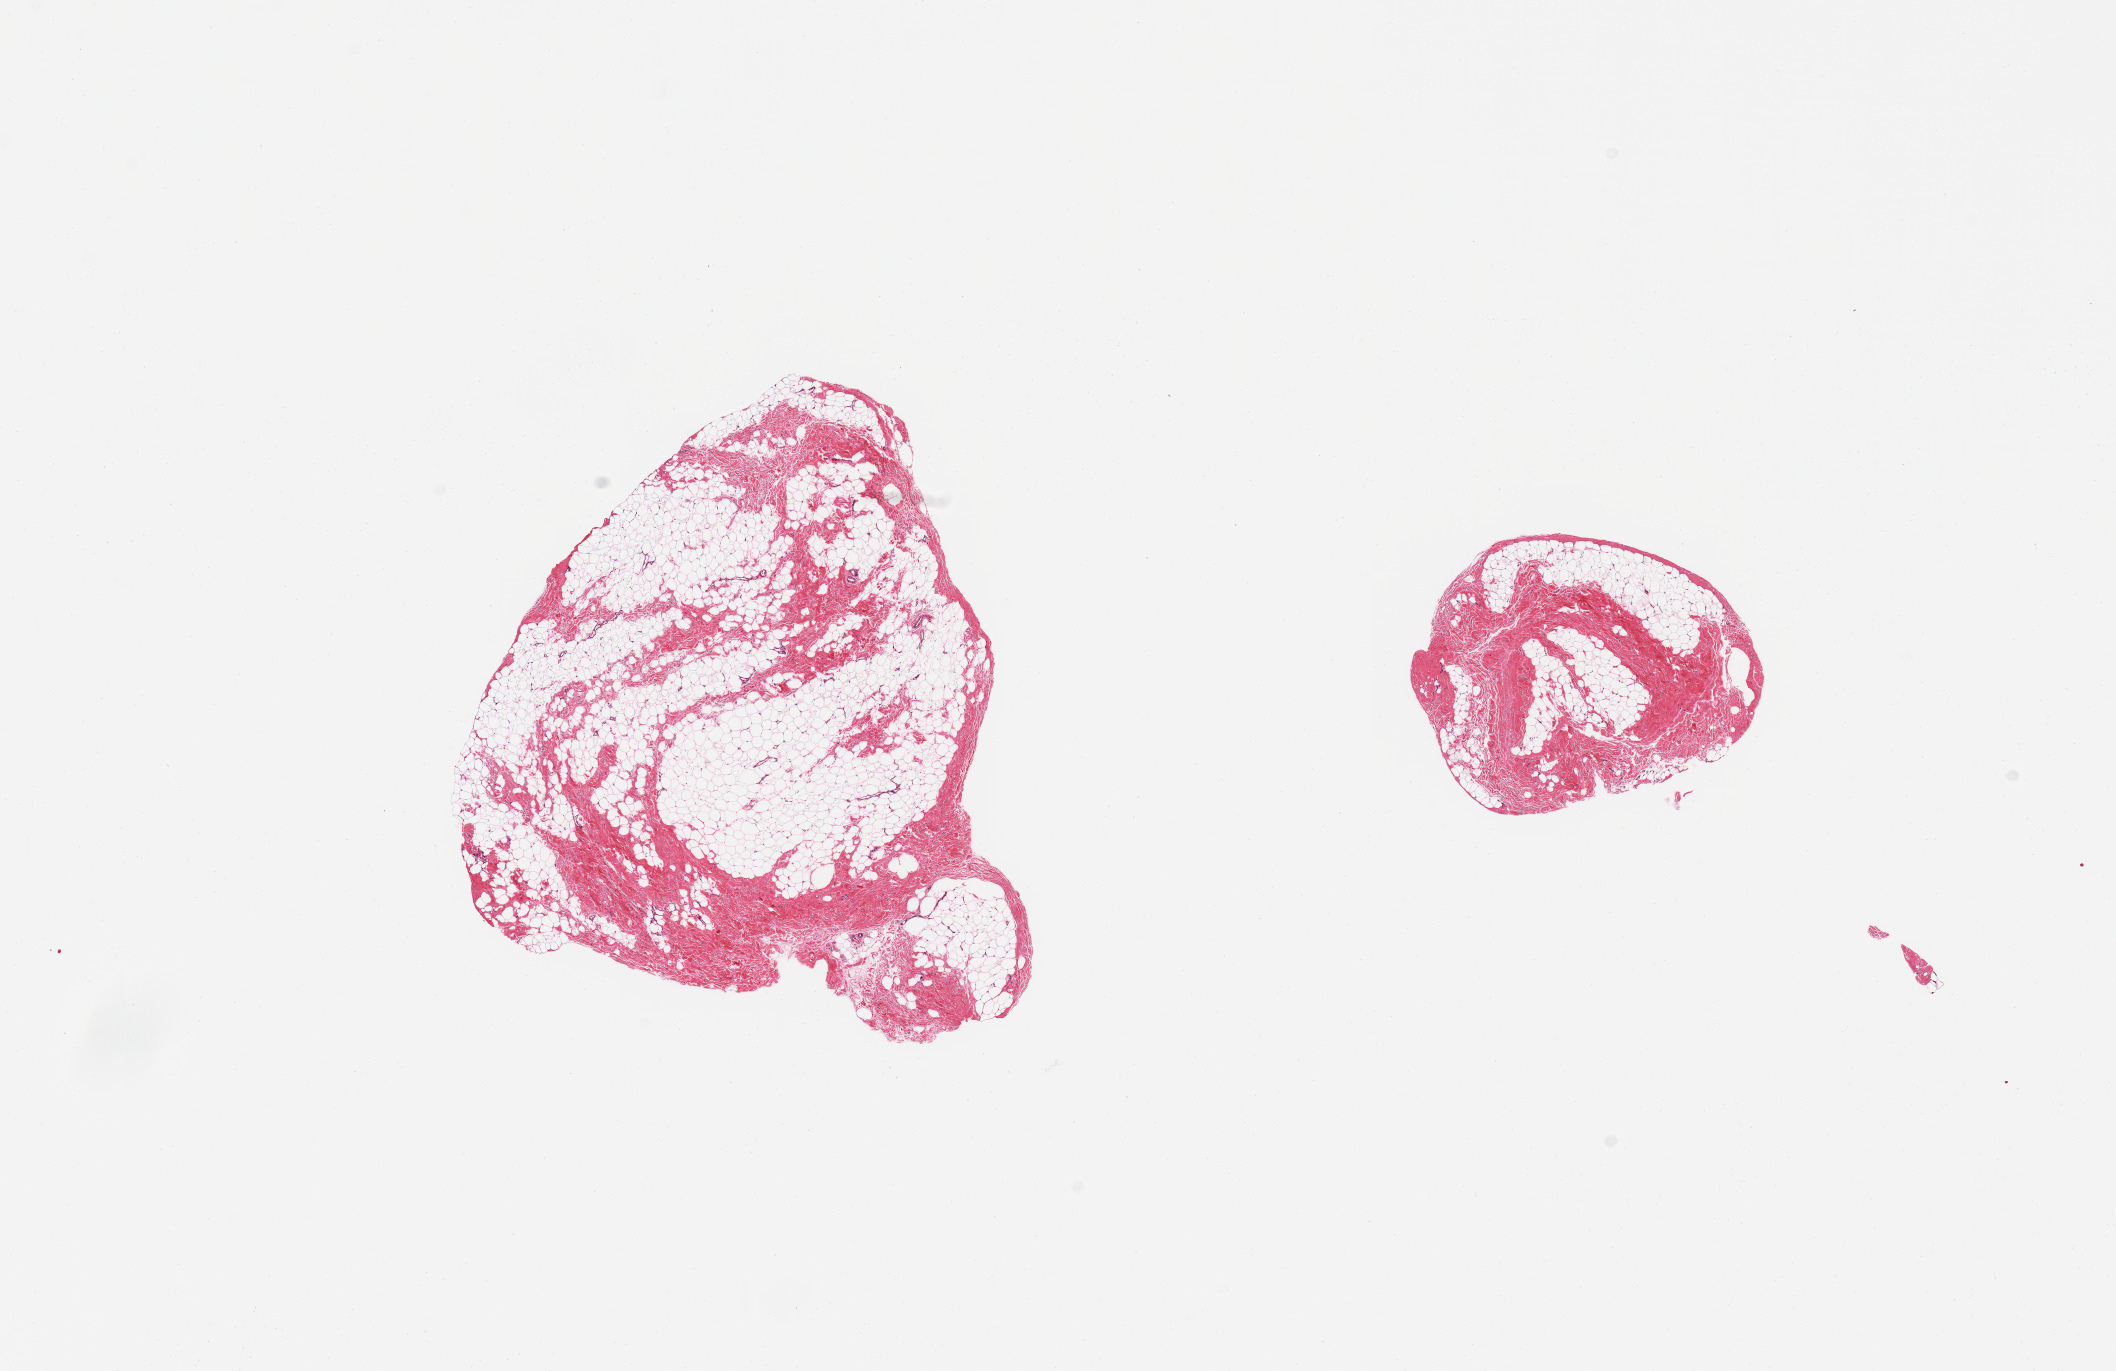
Digitized hematoxylin and eosin (H&E)-stained section, brightfield — a low-resolution overview of the entire scanned area, about 16.7 x 10.8 mm (from a 20x scan). PAXgene-fixed paraffin-embedded (PFPE) section. Sampled site (target tissue): breast. Tissue donor sample. Donor sex: male.
Pathologist's review note for this sample: 2 pieces; fibrofatty tissue without obvious mammary ducts.